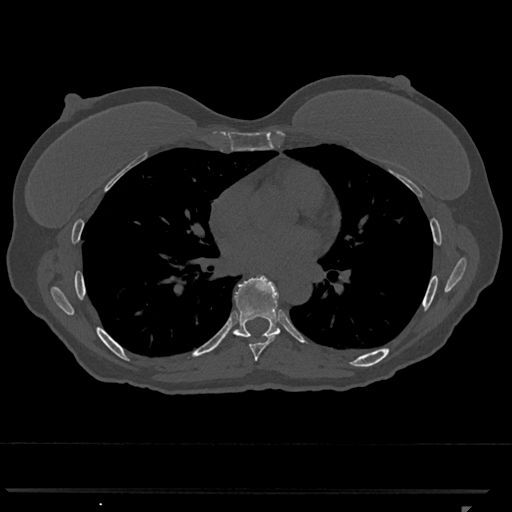
CT including the spine, one axial slice. Position 688 of 793 along the scan axis. 120 kVp. Bone window (W 1800 / L 400 HU). 0.5 mm slice thickness. 512 × 512 image matrix, field of view 380 × 380 mm. Female patient, age 62 years. From the clinical record (not read from this slice): primary cancer: renal.
Structures marked on this image (semi-automatically segmented with operator editing):
- T7 vertebra: bounding box [x1, y1, x2, y2] px = [242, 335, 276, 362]
- T8 vertebra: [233, 276, 281, 337]